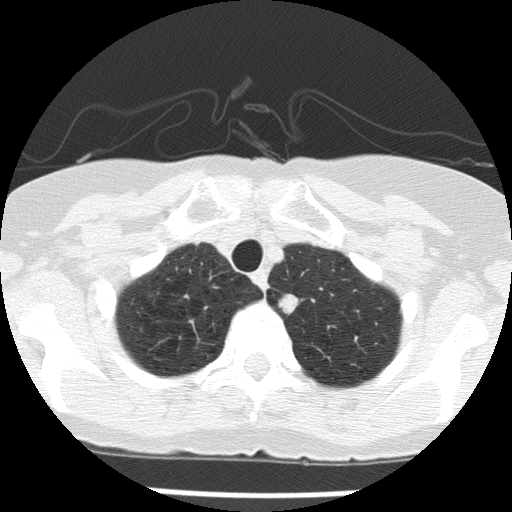
Low-dose screening chest CT, axial slice; baseline annual screen; lung window (W 1500 / L -600 HU); 120 kVp; slice 19 of 143 in the series. Female, age 74 years at enrolment. Former smoker at enrolment.
Lesion marked by an expert reader, box from (x=271, y=289) to (x=306, y=317) px. The screening reader recorded 2 non-calcified nodules or masses ≥4 mm on this exam (left lower lobe, left upper lobe); which of them this box marks is not recorded. Official screen result: positive, change unspecified: nodule(s) >= 4 mm or enlarging nodule(s), mass(es), or other non-specific abnormalities suspicious for lung cancer. Later outcome: lung cancer diagnosed 81 days after this screen — adenocarcinoma, NOS, left upper lobe, poorly differentiated (G3), stage IA (AJCC 6th edition), 24 mm at pathology.